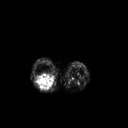
FDG PET of an extremity soft-tissue mass (from a PET/CT study), one axial slice; position 173 of 267 along the scan axis; 3.27 mm slice thickness; 128 × 128 image matrix, field of view 500 × 500 mm. Female patient, age 62 years. From the clinical record (not read from this slice): histological type: liposarcoma; site of the primary tumour: right thigh.
Annotated regions visible in this slice (expert contour drawn on MRI and transferred to this co-registered scan by the dataset authors):
- gross tumour volume (mass): bounding box (x1, y1, x2, y2) in pixels: (36, 72, 56, 90)